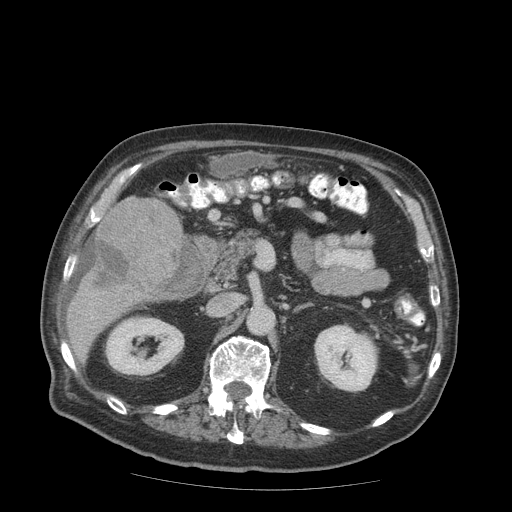
Contrast-enhanced abdominal CT (liver protocol), one axial slice; position 33 of 99 along the scan axis; reconstruction kernel STANDARD; 140 kVp; soft-tissue window (W 400 / L 40 HU); 512 × 512 image matrix, field of view 420 × 420 mm. From the clinical record (not read from this slice): diagnosis: hepatocellular carcinoma (patient treated with transarterial chemoembolisation; whether this scan precedes or follows treatment is not stated here); TNM stage (as recorded): Stage-IIIB; Child-Pugh class: A; tumour differentiation: well differentiated.
Annotated regions visible in this slice (semi-automatically segmented with operator editing):
- liver parenchyma outside the tumour (the mass and vessels are separate outlines, so this box may not span the whole liver): bounding box <68,196,188,350> (left, top, right, bottom; pixels)
- mass: <90,195,184,297>